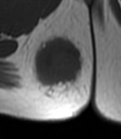
MRI of an extremity soft-tissue mass, one axial slice. Position 18 of 47 along the scan axis. MR volume resampled by the dataset authors to the PET/CT grid (not the native acquisition matrix). 121 × 139 image matrix, field of view 118 × 136 mm. Female patient. Case-level facts recorded for this patient, not image findings: histological type: epithelioid sarcoma; grade: intermediate; site of the primary tumour: right buttock.
Outlined on this slice (expert contour drawn on MRI and transferred to this co-registered scan by the dataset authors):
- gross tumour volume including surrounding oedema: bounding box <29,36,89,108> (left, top, right, bottom; pixels)
- gross tumour volume (mass): <34,41,80,85>